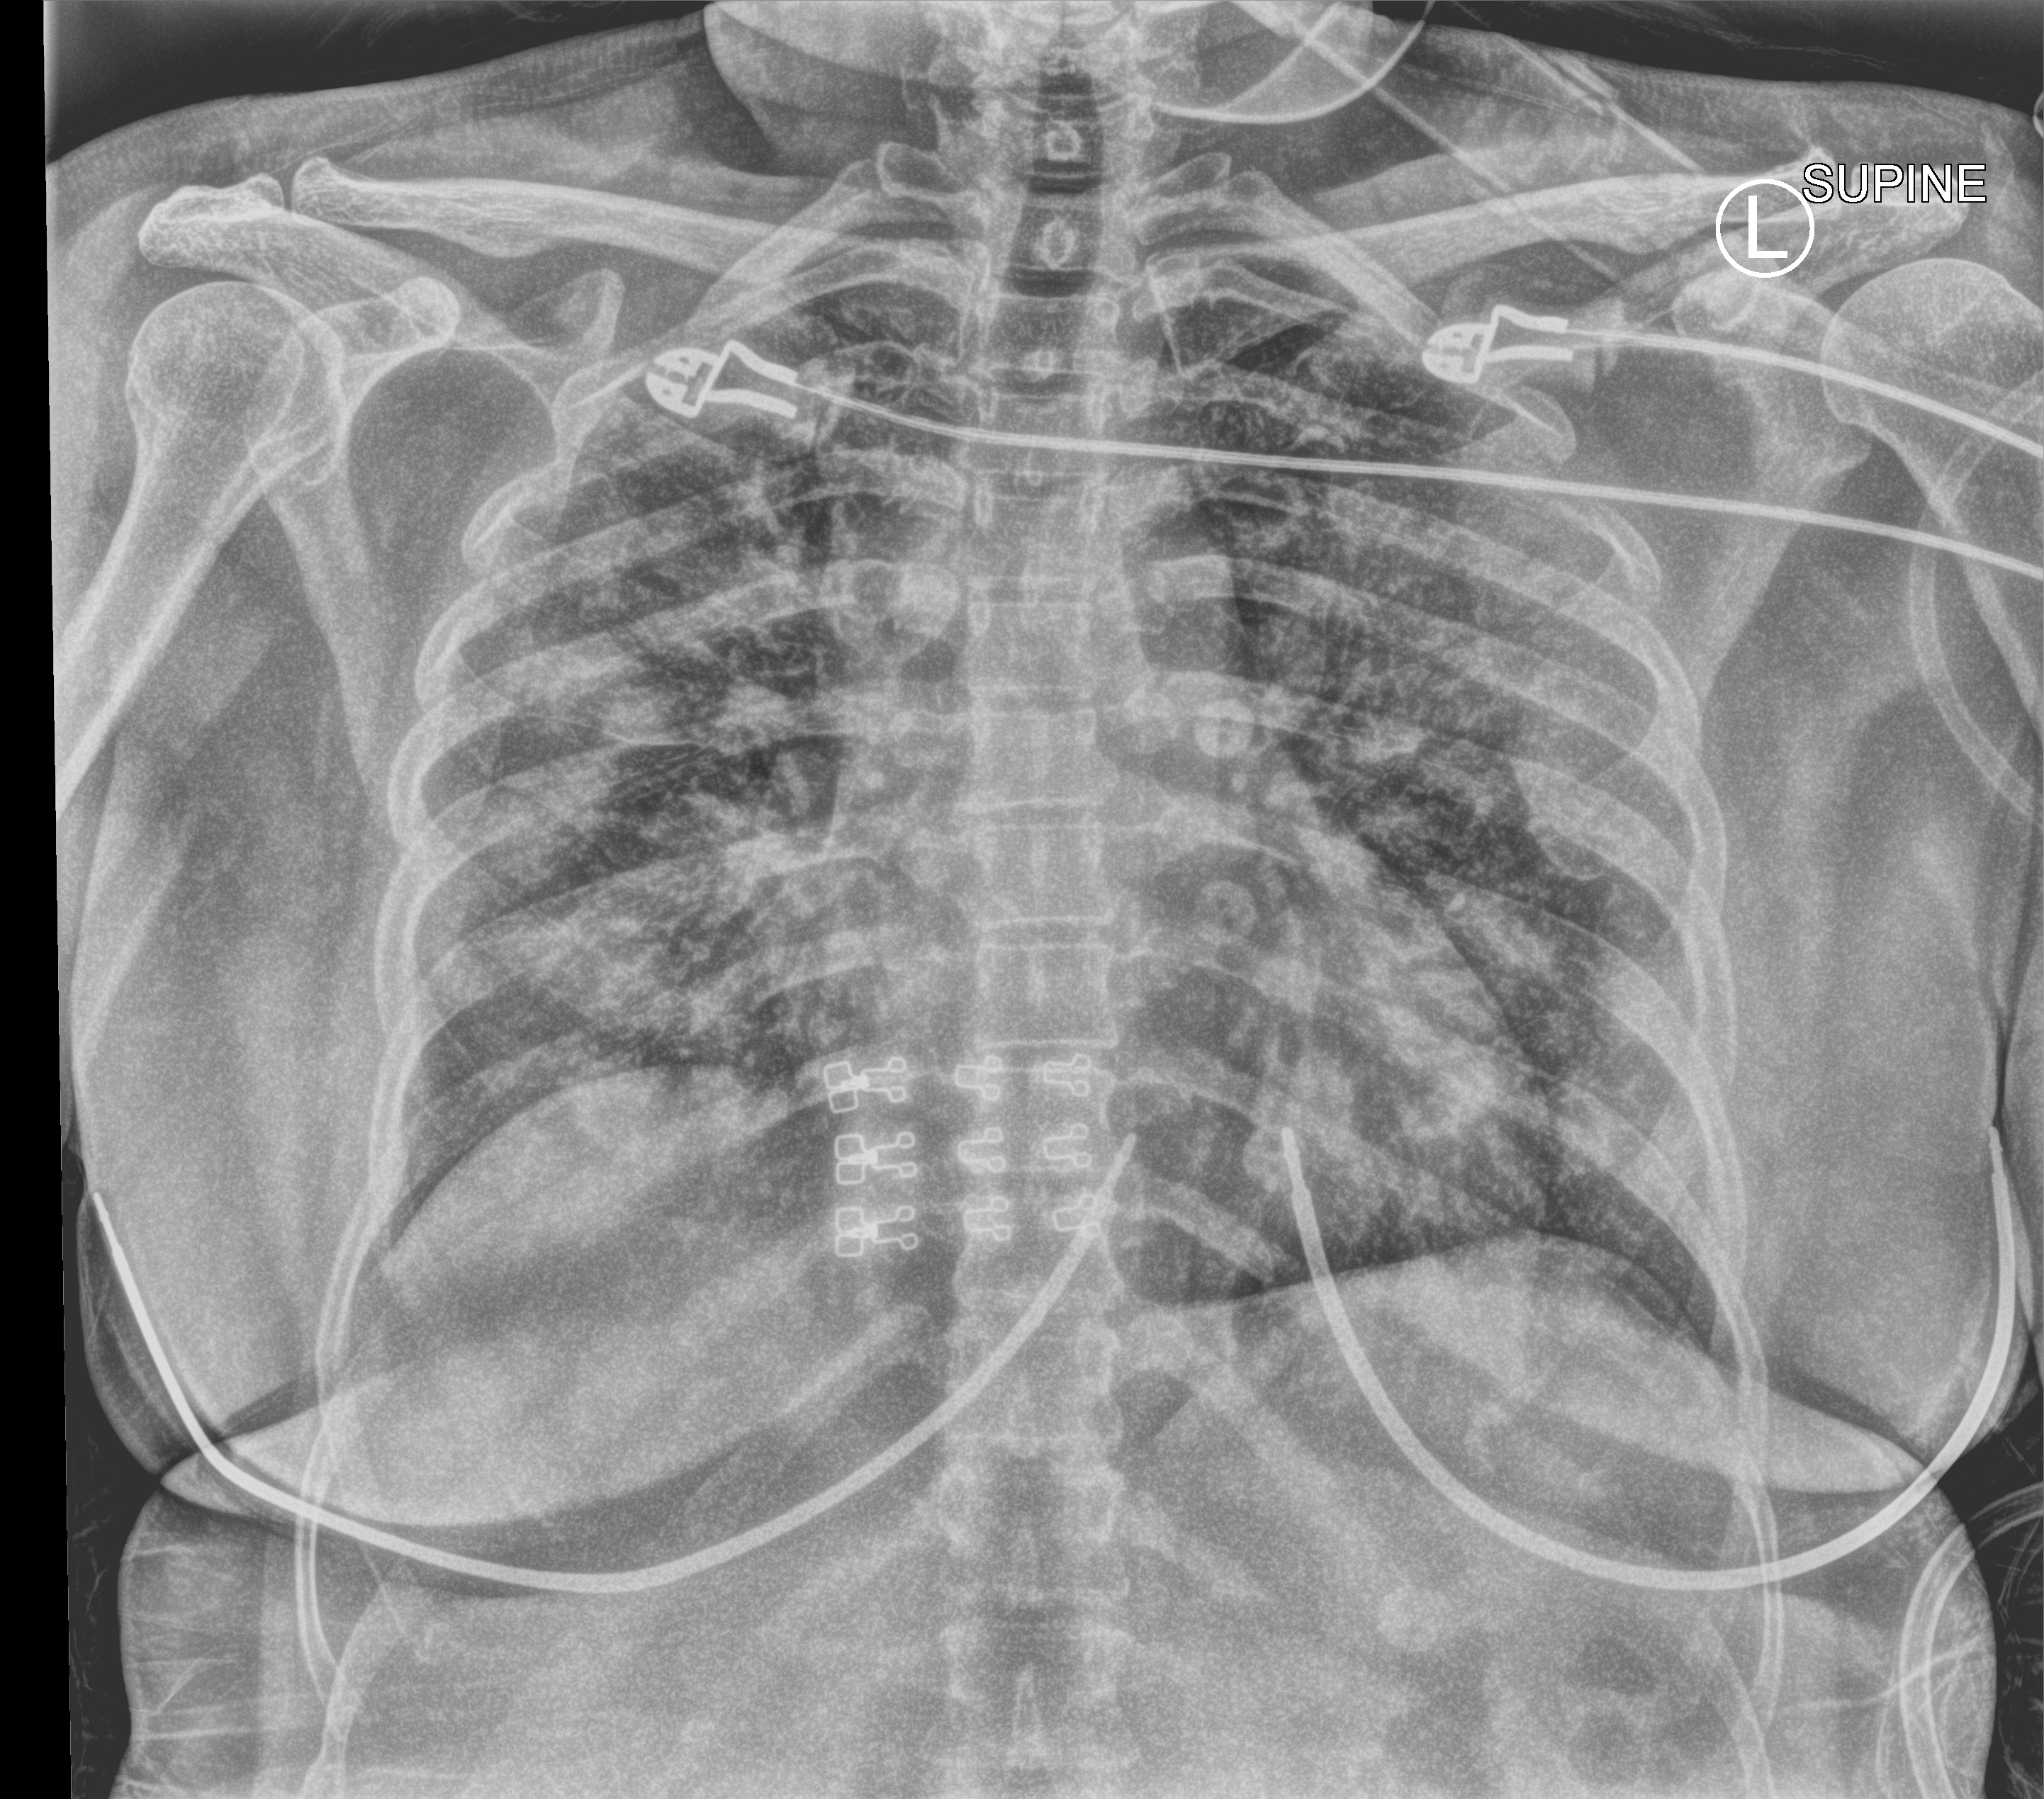
Bedside chest radiograph (computed radiography). Male patient hospitalised with COVID-19, age 18–59 years.
Admission-level facts for this patient (not findings on this image; timing relative to this image not recorded): length of hospital stay: 38 days.